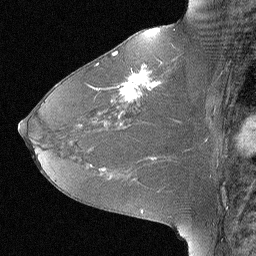
Breast MRI (dynamic contrast-enhanced), one sagittal slice. Slice 36 of 64 in the series (ordered by position). Dynamic contrast-enhanced study with each time point stored as its own series, time point 2 of 3 at this slice position (early post-contrast, ordered by acquisition time). 1.5 T. TE 4 ms, TR 30 ms. 256 × 256 image matrix, field of view 180 × 180 mm. Patient: female, 46 years. Case-level facts recorded for this patient, not image findings: setting: breast cancer imaged before/during neoadjuvant chemotherapy; receptor status: HR-positive, HER2-negative.
Outlined on this slice (semi-automatically segmented with operator editing):
- analysis volume of interest (the breast-tissue region the enhancement analysis was run in; not a lesion): bounding box (x1, y1, x2, y2) in pixels: (106, 43, 184, 119)
- tumour enhancement mask (voxels above the 90 % enhancement threshold inside the analysis volume of interest): (112, 52, 162, 102)